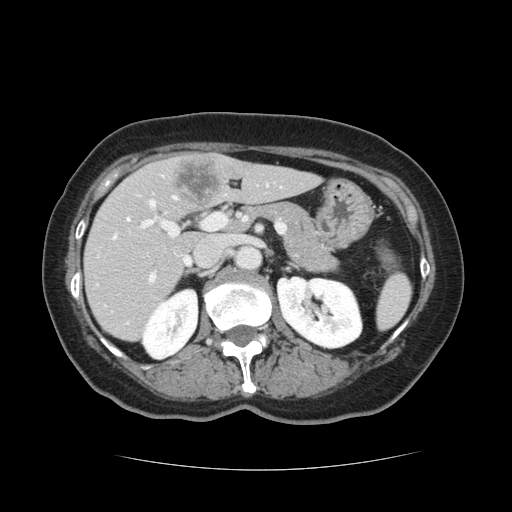
Contrast-enhanced abdominal CT, one axial slice. Position 65 of 128 along the scan axis. 120 kVp. Intravenous contrast given. Soft-tissue window (W 400 / L 40 HU). 2.5 mm slice thickness. 512 × 512 image matrix, field of view 366 × 366 mm. Female patient, age 67 years. From the clinical record (not read from this slice): diagnosis: colorectal cancer liver metastases, imaged before liver resection; multiple liver metastases: yes; largest metastasis: 3 cm; chemotherapy before resection: no.
Annotated regions visible in this slice (expert manual segmentation):
- hepatic veins: bounding box (x1, y1, x2, y2) in pixels: (114, 196, 190, 264)
- liver: (85, 154, 318, 341)
- planned liver remnant (the part of the liver to remain after resection): (85, 163, 318, 341)
- portal vein (with intrahepatic branches): (140, 182, 275, 284)
- liver metastasis: (175, 160, 219, 205)